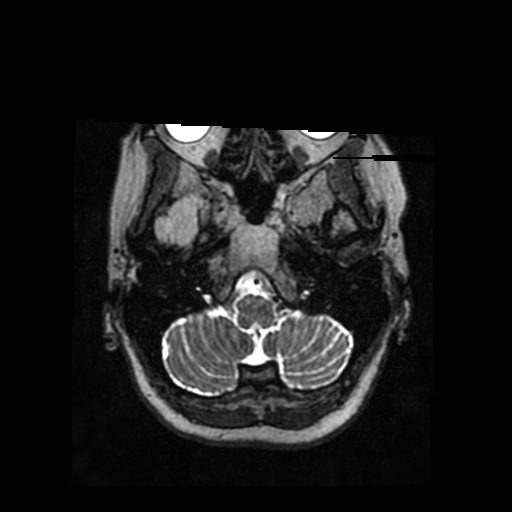
Brain MRI from a brain-tumour surgery series, one axial slice. Slice 191 of 290 in the series (ordered by position). 0.83 mm slice thickness. 512 × 512 image matrix, field of view 240 × 240 mm. From the clinical record (not read from this slice): histopathology: Glioblastoma; WHO grade: 4; IDH mutation: no; tumour location: Right Anterior Temporal.
Structures marked on this image (outlined manually by an expert reader):
- tumour: box from (x=189, y=197) to (x=207, y=225) px